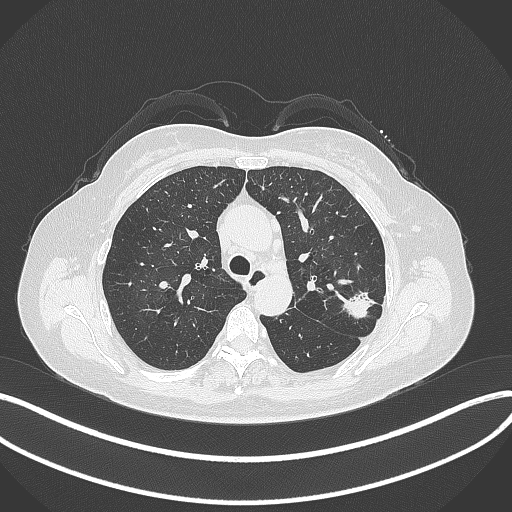
Chest CT, one axial slice. Position 226 of 319 along the scan axis. 120 kVp. Lung window (W 1500 / L -600 HU). 1 mm slice thickness. 512 × 512 image matrix, field of view 400 × 400 mm. Patient: female, 60 years. From the clinical record (not read from this slice): clinical TNM (as recorded): T1c N0 M0.
Outlined on this slice (rectangle marked by the reading radiologist):
- lung tumour (recorded histology: adenocarcinoma): bounding box <337,285,376,323> (left, top, right, bottom; pixels)